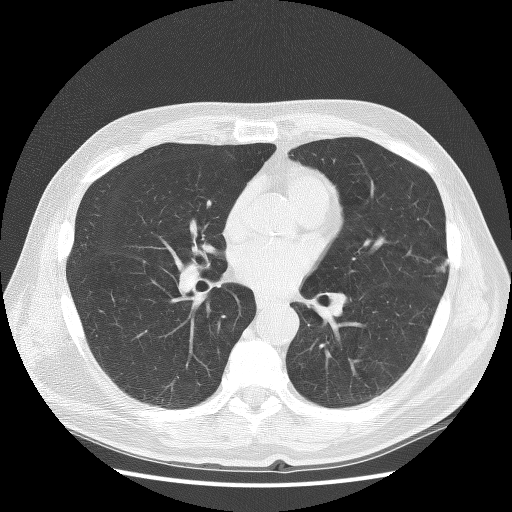
Low-dose screening chest CT, axial slice. First (baseline) screen. Lung window (W 1500 / L -600 HU). 2.5 mm slice thickness. Lung (sharp) reconstruction kernel (BONE). 120 kVp. Male, age 67 years at enrolment. Former smoker at enrolment.
- Expert reader's lesion annotation, bounding box (x1, y1, x2, y2) in pixels: (403, 244, 463, 296).
- Screening reader's record for this exam: no non-calcified nodule ≥4 mm recorded.